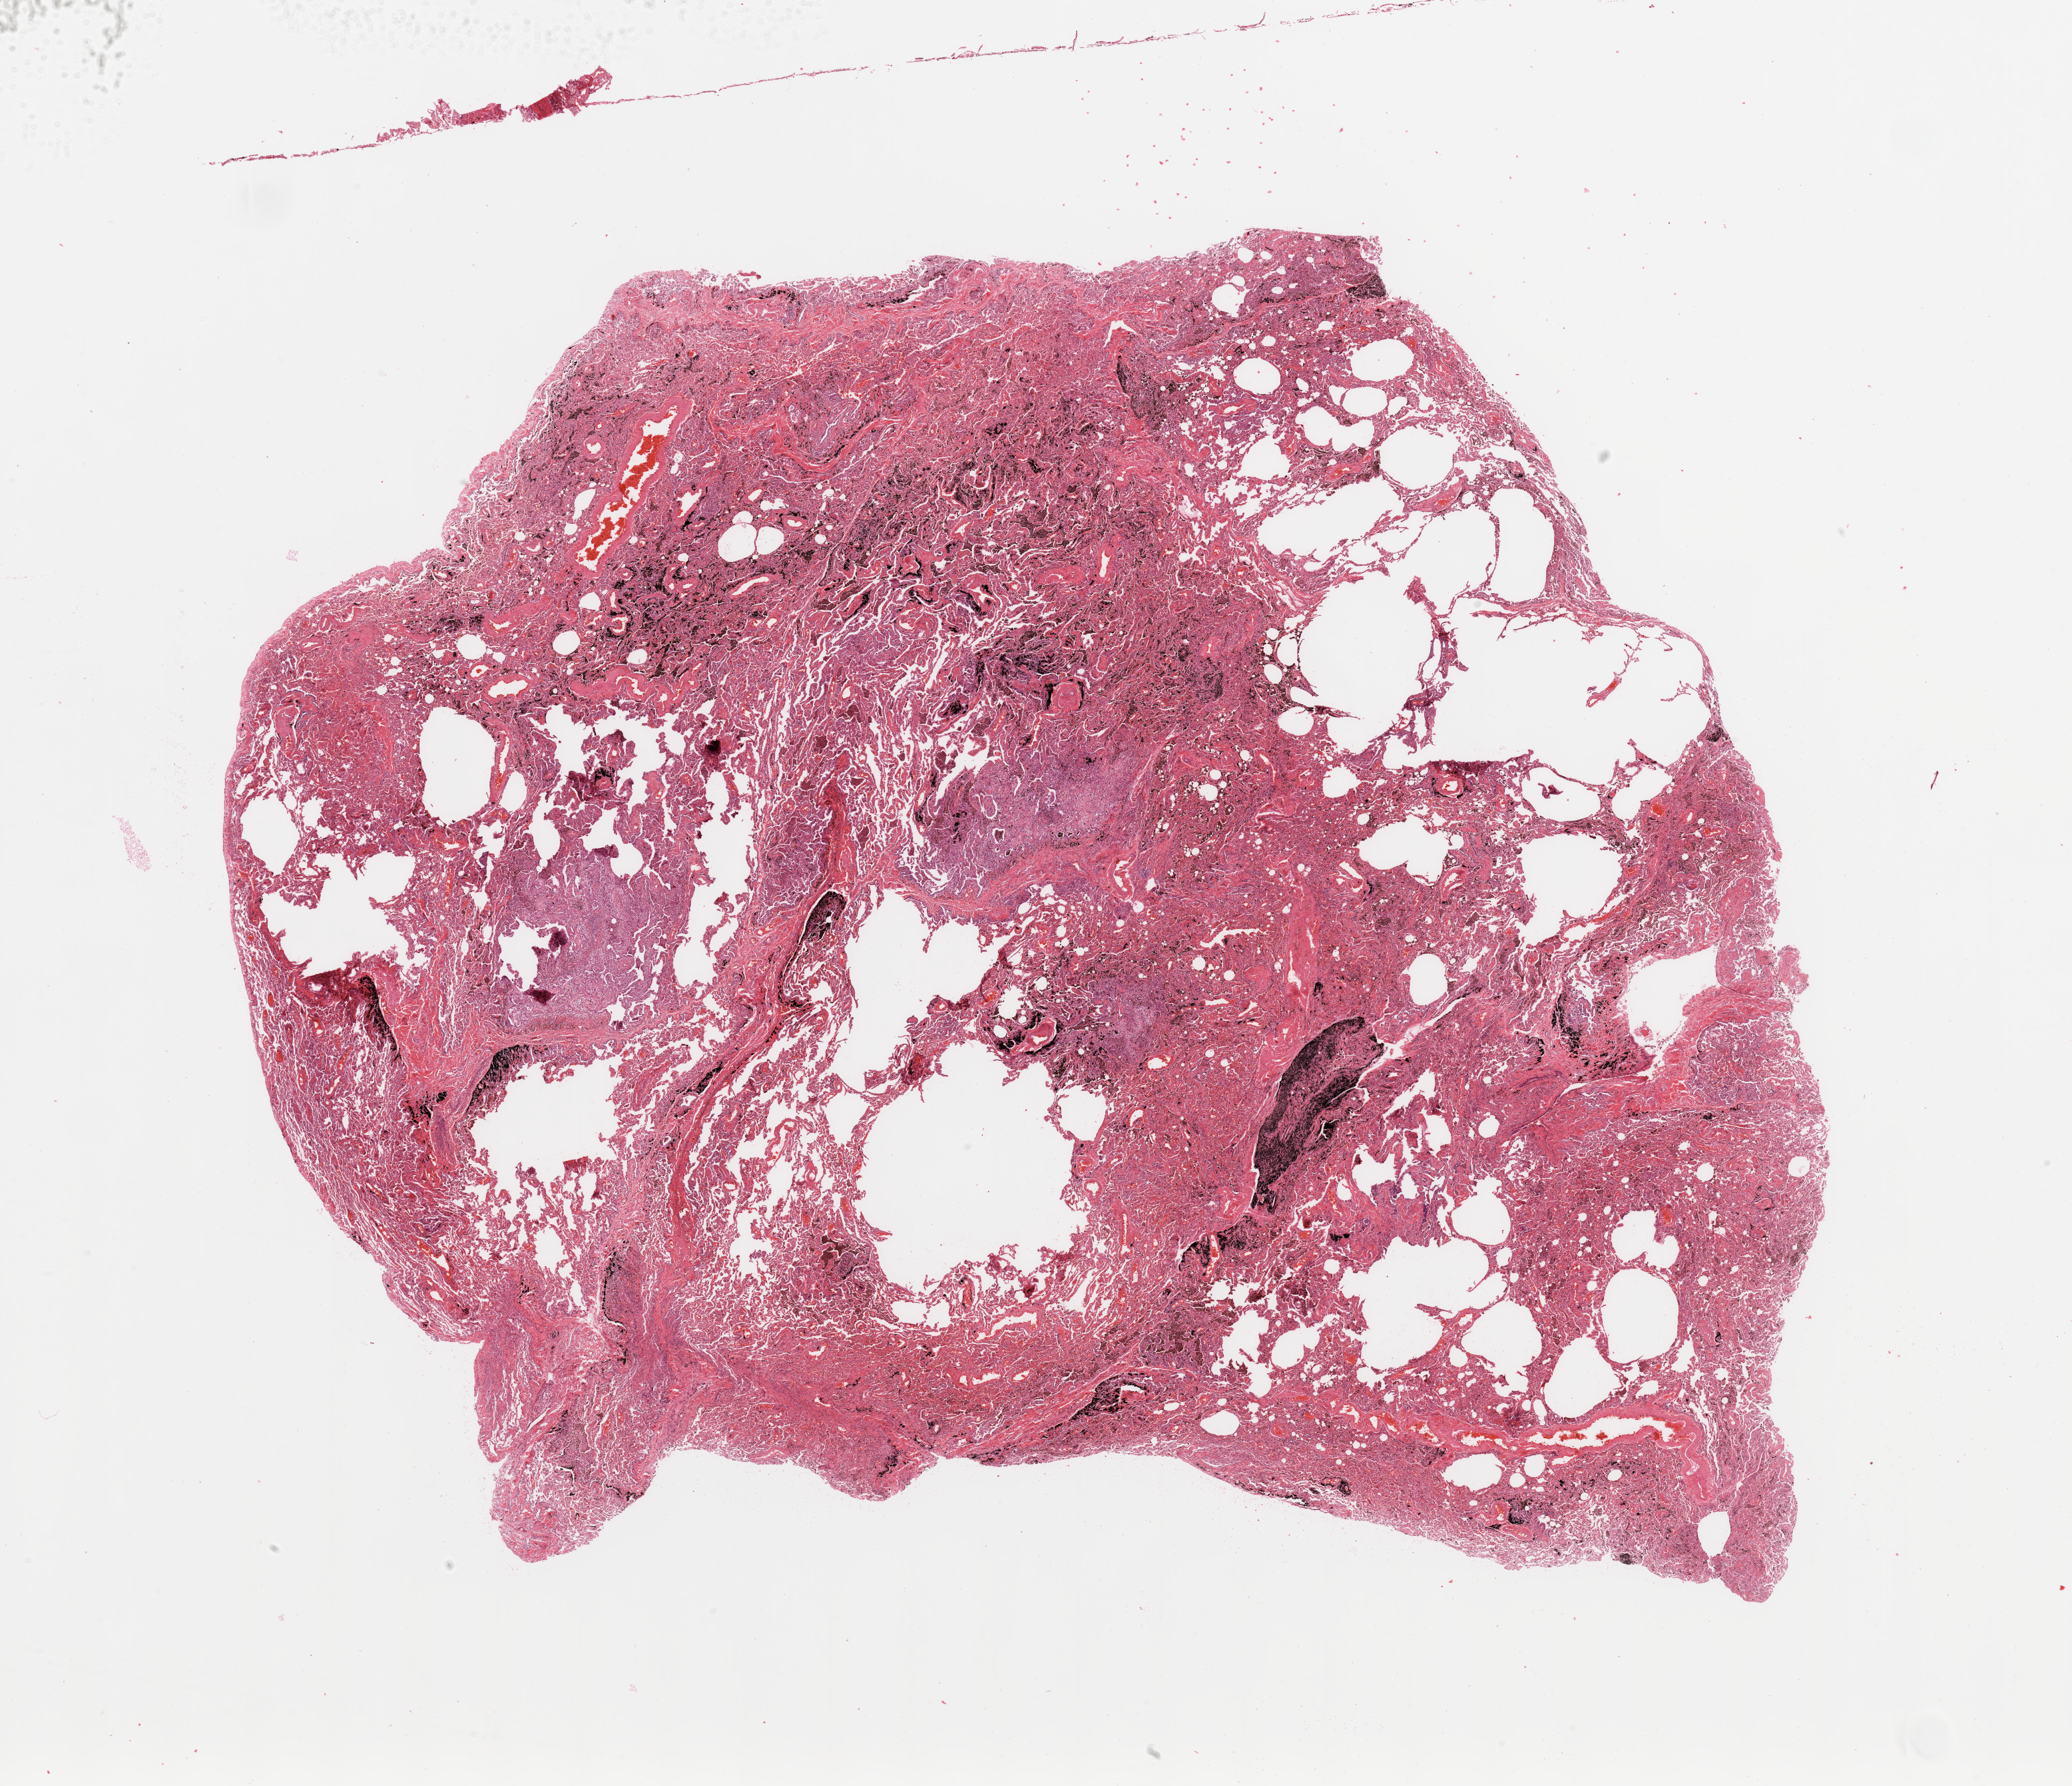
Hematoxylin and eosin (H&E) stained whole-slide image — whole scanned area (about 24.6 x 21.2 mm) shown as a low-resolution overview. Lung, normal (non-tumour) tissue. Male, 60 y/o.
This section: normal (non-tumour) tissue from the same patient. Patient diagnosis: Adenocarcinoma, NOS.